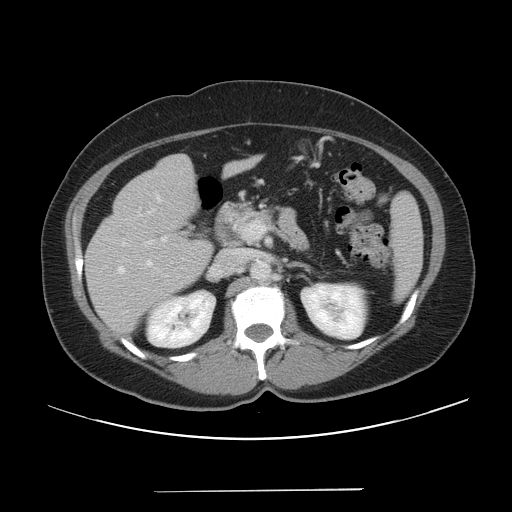
Contrast-enhanced abdominal CT, one axial slice. Slice 23 of 56 in the series (ordered by position). 120 kVp. Intravenous contrast given. Soft-tissue window (W 400 / L 40 HU). 5 mm slice thickness. 512 × 512 image matrix, field of view 419 × 419 mm. Female patient, age 54 years. Case-level facts recorded for this patient, not image findings: diagnosis: colorectal cancer liver metastases, imaged before liver resection.
Outlined on this slice (outlined manually by an expert reader):
- hepatic veins: bounding box <118,261,151,273> (left, top, right, bottom; pixels)
- liver: <84,154,257,335>
- planned liver remnant (the part of the liver to remain after resection): <161,154,258,200>
- portal vein (with intrahepatic branches): <148,221,266,244>